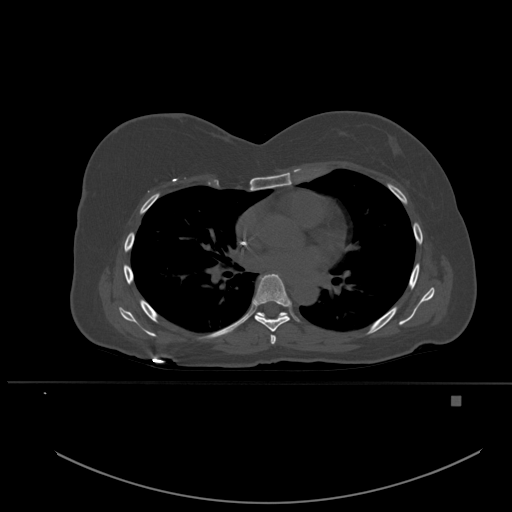
CT including the spine, one axial slice; slice 347 of 651 in the series (ordered by position); bone window (W 1800 / L 400 HU); 512 × 512 image matrix, field of view 443 × 443 mm. Patient: female, 49 years. Case-level facts recorded for this patient, not image findings: primary cancer: breast; vertebrae with lytic lesions (as recorded): L3, T12, L4.
Annotated regions visible in this slice (semi-automatically segmented with operator editing):
- T5 vertebra: bounding box <270,335,276,344> (left, top, right, bottom; pixels)
- T6 vertebra: <253,274,291,332>
- T7 vertebra: <256,312,288,318>